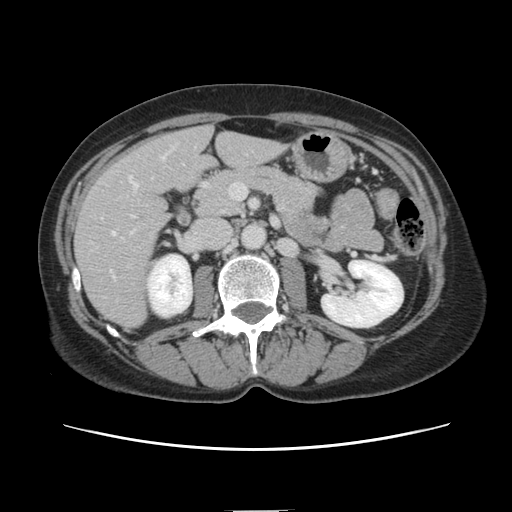
Contrast-enhanced abdominal CT, one axial slice. Position 55 of 141 along the scan axis. Intravenous contrast given. Soft-tissue window (W 400 / L 40 HU). 2.5 mm slice thickness. 512 × 512 image matrix, field of view 350 × 350 mm. Female patient, age 63 years. Case-level facts recorded for this patient, not image findings: diagnosis: colorectal cancer liver metastases, imaged before liver resection; multiple liver metastases: yes; largest metastasis: 3.2 cm; disease in both lobes: yes.
Structures marked on this image (outlined manually by an expert reader):
- hepatic veins: bounding box (x1, y1, x2, y2) in pixels: (113, 157, 164, 234)
- liver: (76, 127, 282, 328)
- planned liver remnant (the part of the liver to remain after resection): (177, 128, 282, 182)